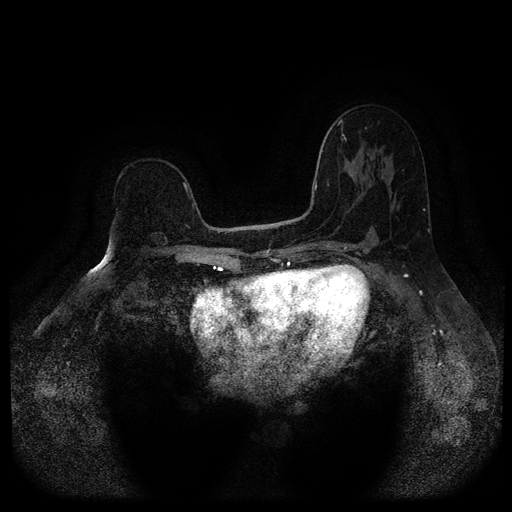
Breast MRI (dynamic contrast-enhanced, multi-phase), one axial slice. Position 65 of 116 along the scan axis. Dynamic contrast-enhanced series, time point 2 of 5 at this slice position (early post-contrast). 1.5 T. TE 2.6 ms, TR 5.4 ms. 2 mm slice thickness. 512 × 512 image matrix, field of view 340 × 340 mm. Female patient, age 64 years.
Outlined on this slice (semi-automatically segmented with operator editing):
- breast lesion (labelled benign in the annotation): bounding box (x1, y1, x2, y2) in pixels: (150, 232, 169, 252)